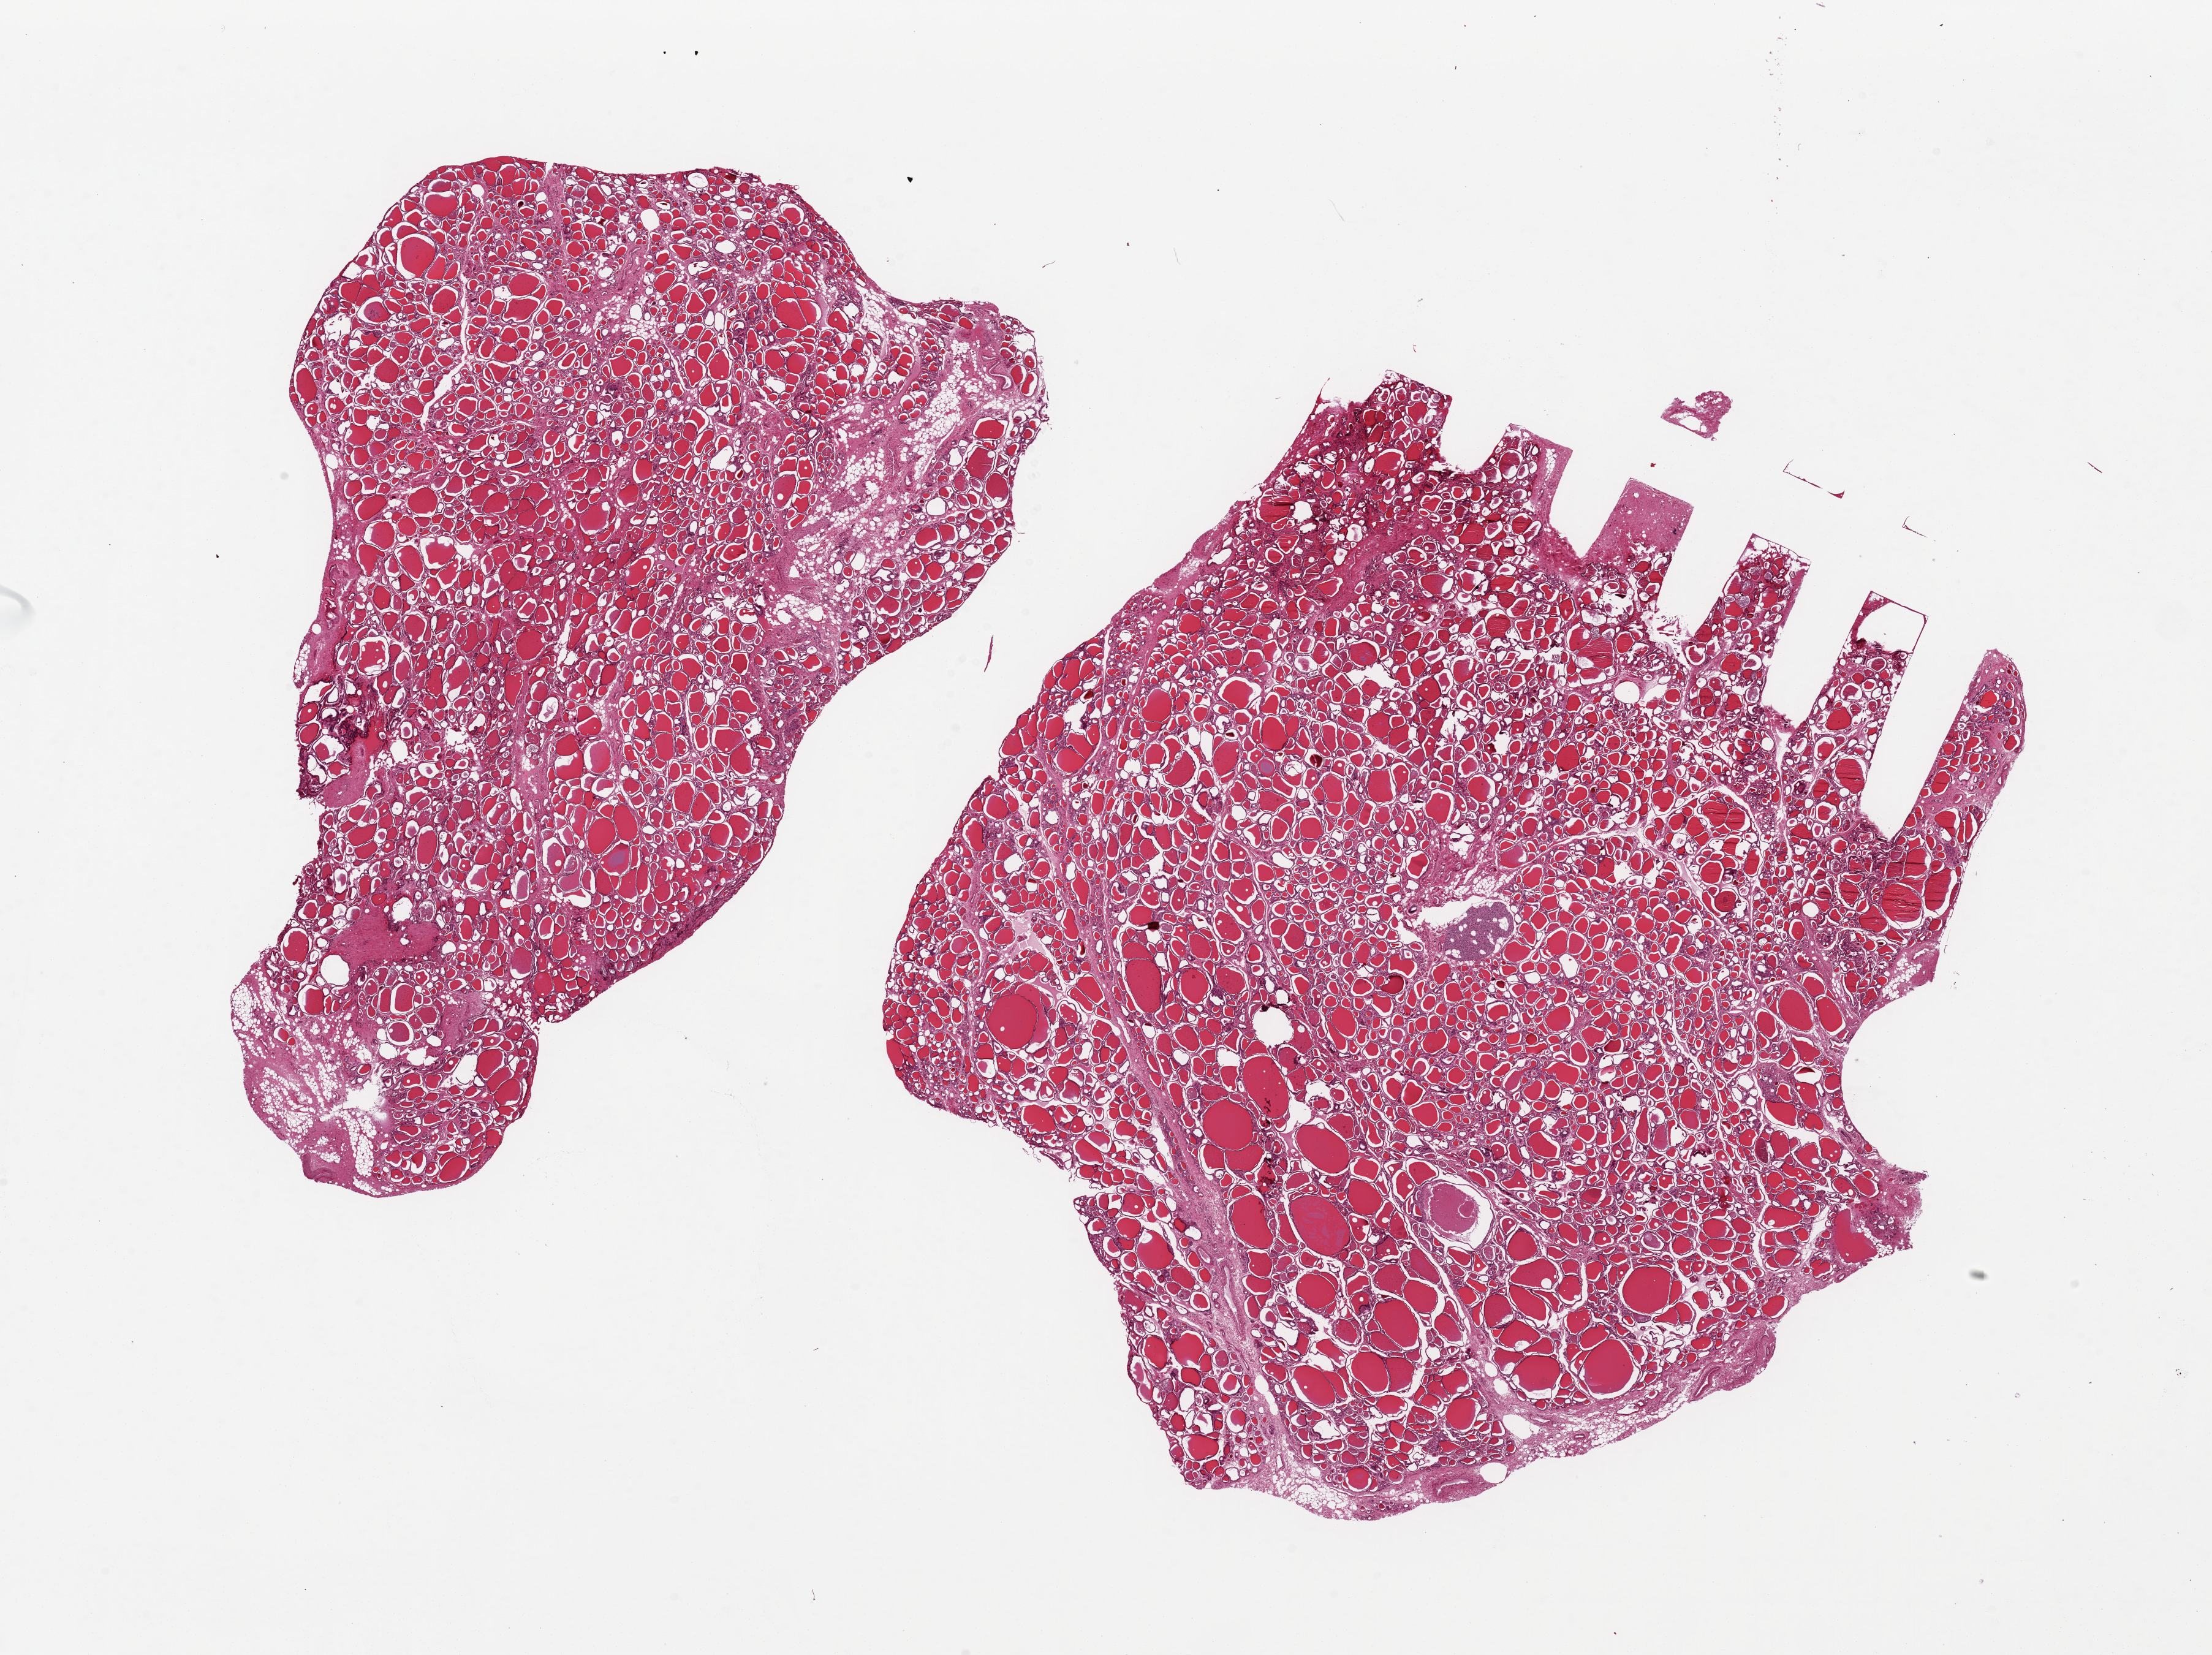
H&E whole-slide image, brightfield — shown as a low-resolution overview of the whole scanned area (about 28.5 x 21.4 mm, slide scanned at 20x), PAXgene-fixed paraffin-embedded (PFPE) section, sampled site (target tissue): thyroid, donor tissue sample. Donor: female.
Reviewer comment on this tissue sample: 2 pieces, 14x9 & 15x13mm; ~1mm parathyroid gland embedded in one aliquot.